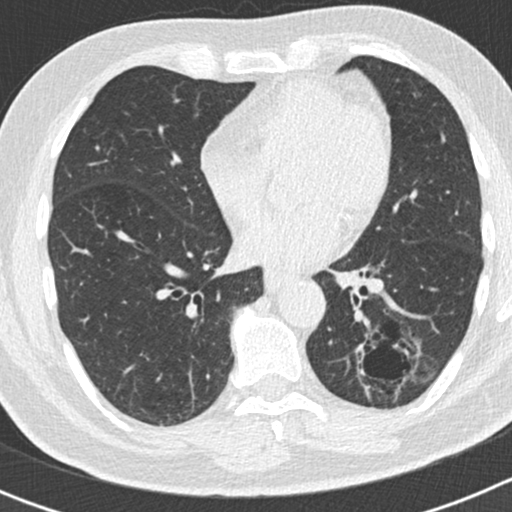
Axial slice from a low-dose chest CT screening exam, second annual screen, lung window (W 1500 / L -600 HU), 2 mm slice thickness, standard (soft-tissue) reconstruction kernel (B30f), slice 96 of 186 in the series. Male participant, aged 66 years at enrolment. Former smoker at enrolment.
Lesion marked by an expert reader, box from (x=348, y=329) to (x=415, y=404) px. Screening reader's record for this exam (one nodule recorded; not confirmed to be the boxed lesion): non-calcified nodule or mass ≥4 mm, left lower lobe, 50 × 33 mm, smooth margins, pre-existing on the prior screen: yes; interval growth: yes. Official screen result: positive, other. Lung cancer was diagnosed 440 days after this screen (after the third annual screen): adenocarcinoma, NOS, left lower lobe, poorly differentiated (G3), stage IB (AJCC 6th edition), 38 mm at pathology.